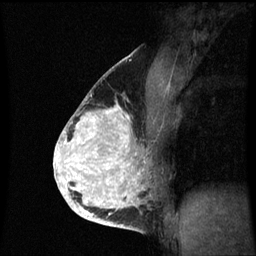
Breast MRI (dynamic contrast-enhanced), one sagittal slice. Slice 39 of 60 in the series (ordered by position). Dynamic contrast-enhanced series, image 2 of 3 at this slice position (ordered by acquisition). 1.5 T. TE 4.2 ms, TR 8.9 ms. 2 mm slice thickness. 256 × 256 image matrix, field of view 200 × 200 mm. Patient: female, 35 years. From the clinical record (not read from this slice): setting: breast cancer imaged before/during neoadjuvant chemotherapy; receptor status: HR-positive, HER2-negative.
Structures marked on this image (semi-automatic segmentation, software-assisted and operator-edited):
- analysis volume of interest (the breast-tissue region the enhancement analysis was run in; not a lesion): box from (x=66, y=96) to (x=158, y=215) px
- tumour enhancement mask (voxels above the 70 % enhancement threshold inside the analysis volume of interest): (x=66, y=104)–(x=144, y=215)